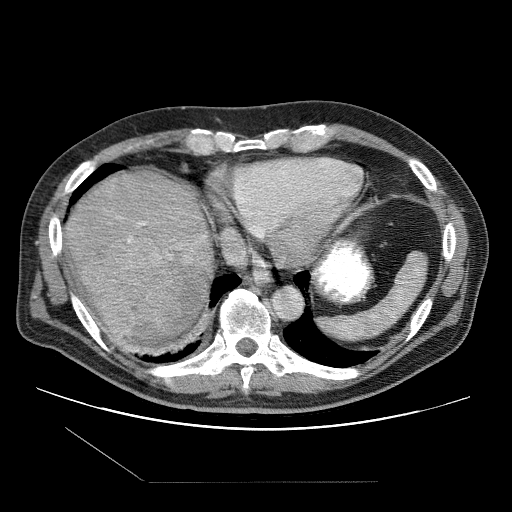
Contrast-enhanced abdominal CT (liver protocol), one axial slice. Slice 90 of 109 in the series (ordered by position). Reconstruction kernel STANDARD. 120 kVp. One of 2 acquisitions stored at this slice position. Soft-tissue window (W 400 / L 40 HU). 2.5 mm slice thickness. 512 × 512 image matrix, field of view 400 × 400 mm. Case-level facts recorded for this patient, not image findings: diagnosis: hepatocellular carcinoma (patient treated with transarterial chemoembolisation; whether this scan precedes or follows treatment is not stated here); TNM stage (as recorded): Stage-IIIB; Child-Pugh class: A.
Annotated regions visible in this slice (semi-automatic segmentation, software-assisted and operator-edited):
- liver parenchyma outside the tumour (the mass and vessels are separate outlines, so this box may not span the whole liver): bounding box (x1, y1, x2, y2) in pixels: (64, 174, 212, 352)
- mass: (82, 233, 183, 336)
- liver vessels: (138, 222, 205, 257)